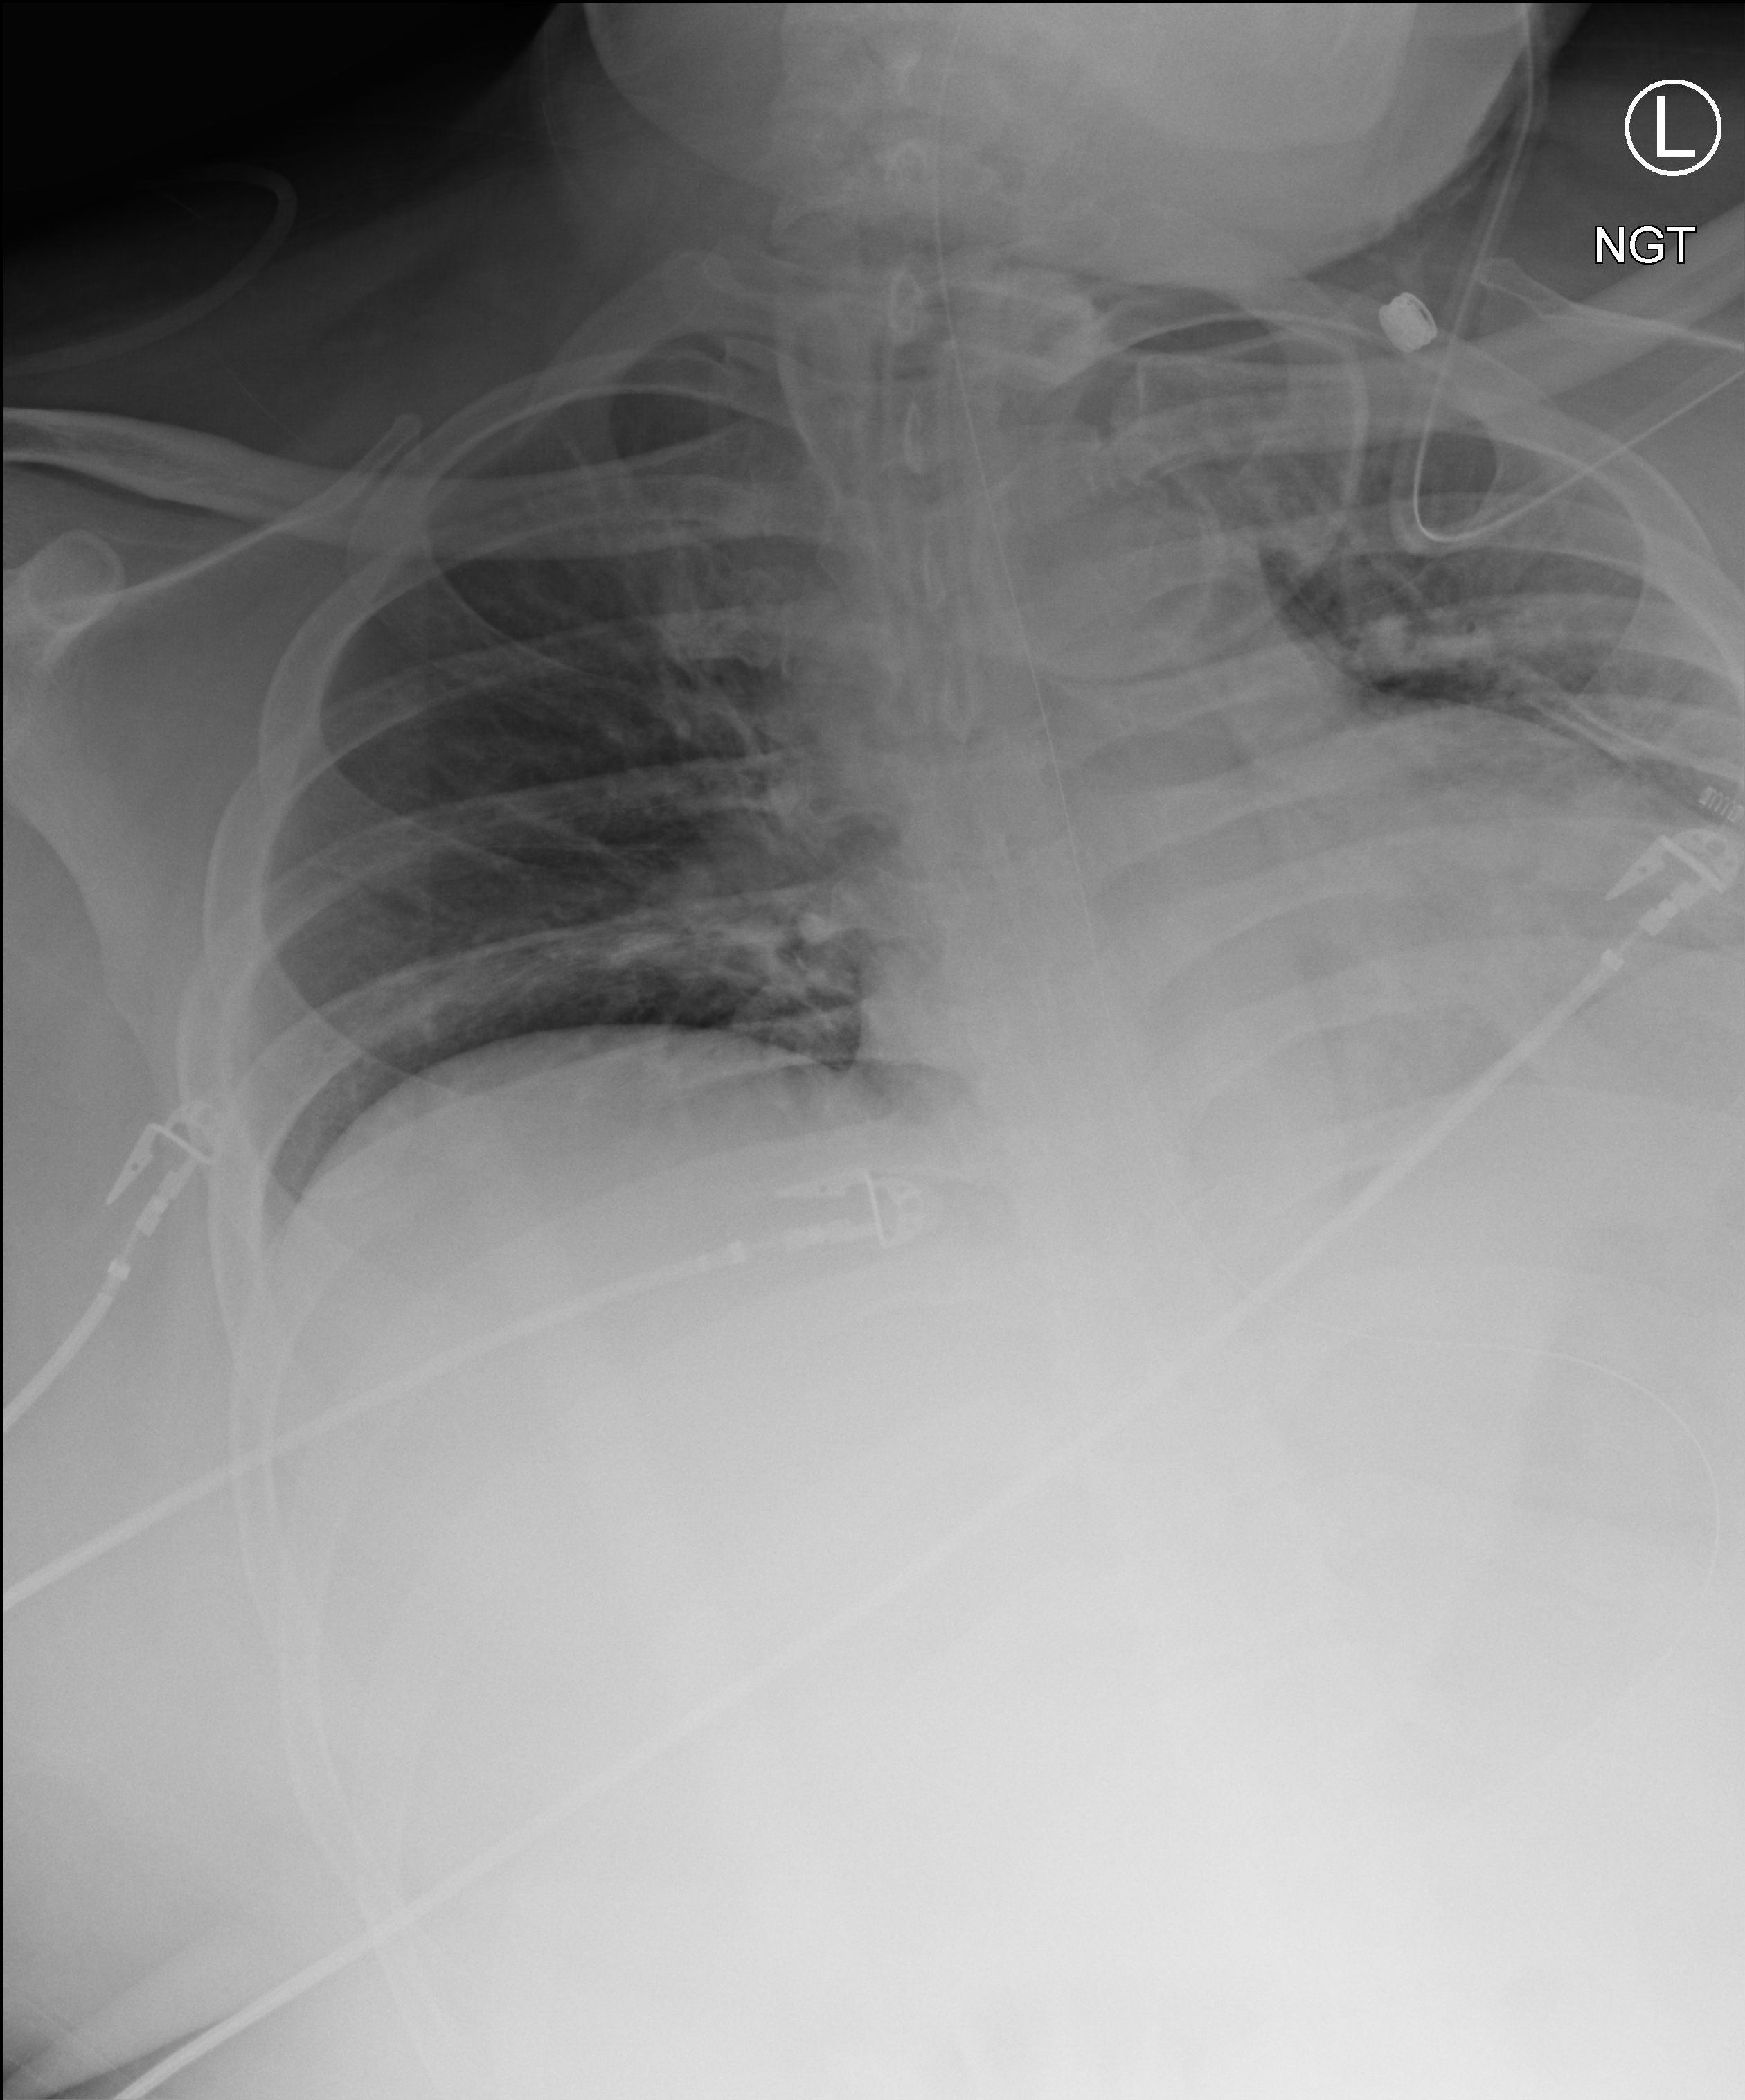
Bedside chest radiograph (computed radiography). Patient hospitalised with COVID-19; male, aged 18–59 years.
Admission-level facts for this patient (not findings on this image; timing relative to this image not recorded):
- admitted to intensive care during this hospital stay: yes
- other chronic lung disease (admission record): yes